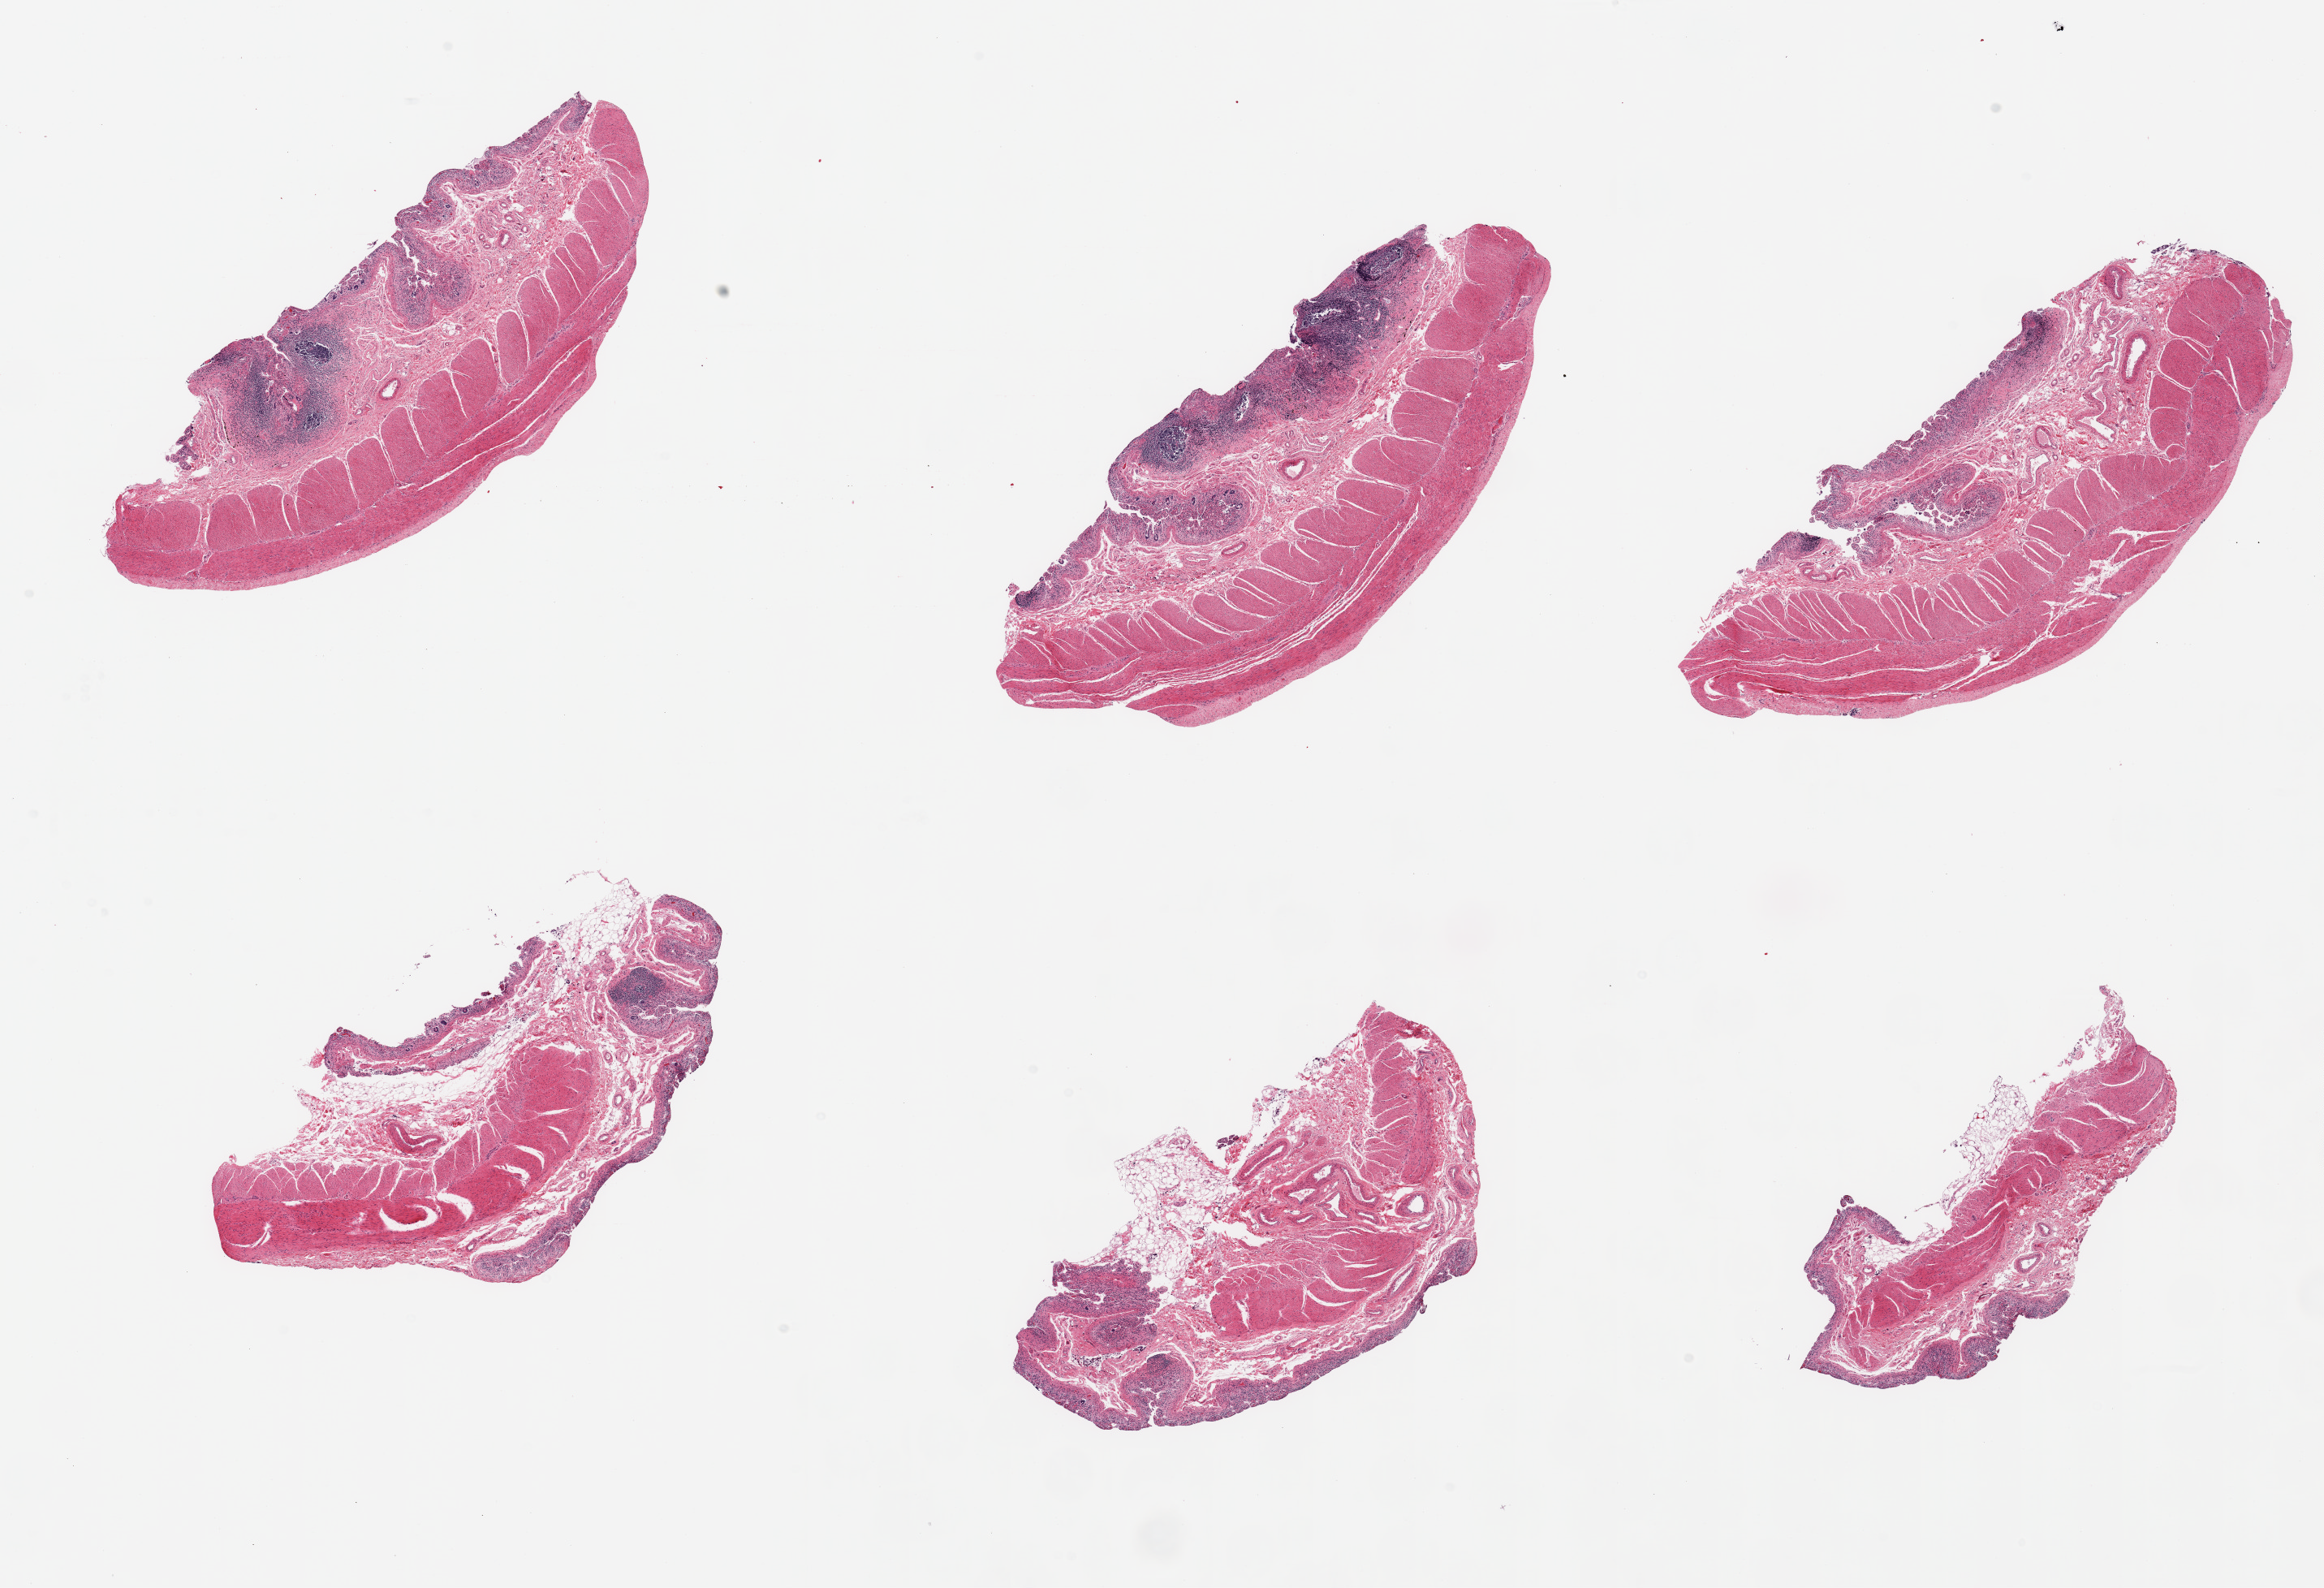
Haematoxylin and eosin whole-slide image — shown as a low-resolution overview of the whole scanned area (about 22.6 x 15.5 mm); PAXgene-fixed paraffin-embedded (PFPE) section; section of ileum (target tissue); donor tissue sample. Donor sex: male.
Review note (as recorded): 6 pieces; autolyzed mucosa and scattered residual lymphoid aggregates in 4 of 6 pieces; muscularis (not target) well preserved.